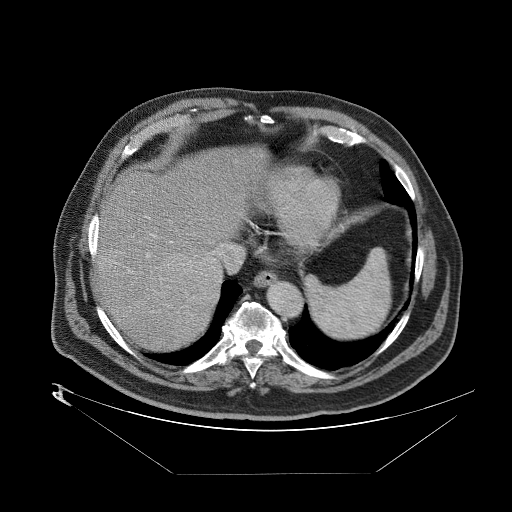
Contrast-enhanced abdominal CT (liver protocol), one axial slice. Slice 70 of 89 in the series (ordered by position). Reconstruction kernel STANDARD. 140 kVp. One of 2 acquisitions stored at this slice position. Soft-tissue window (W 400 / L 40 HU). 512 × 512 image matrix. From the clinical record (not read from this slice): diagnosis: hepatocellular carcinoma (patient treated with transarterial chemoembolisation; whether this scan precedes or follows treatment is not stated here); TNM stage (as recorded): Stage-II; Child-Pugh class: B; tumour differentiation: moderately differentiated; tumour size: 4 cm.
Annotated regions visible in this slice (semi-automatic segmentation, software-assisted and operator-edited):
- abdominal aorta: box from (x=268, y=283) to (x=302, y=317) px
- liver parenchyma outside the tumour (the mass and vessels are separate outlines, so this box may not span the whole liver): (x=90, y=148)–(x=268, y=344)
- mass: (x=156, y=252)–(x=219, y=313)
- liver vessels: (x=132, y=235)–(x=186, y=314)